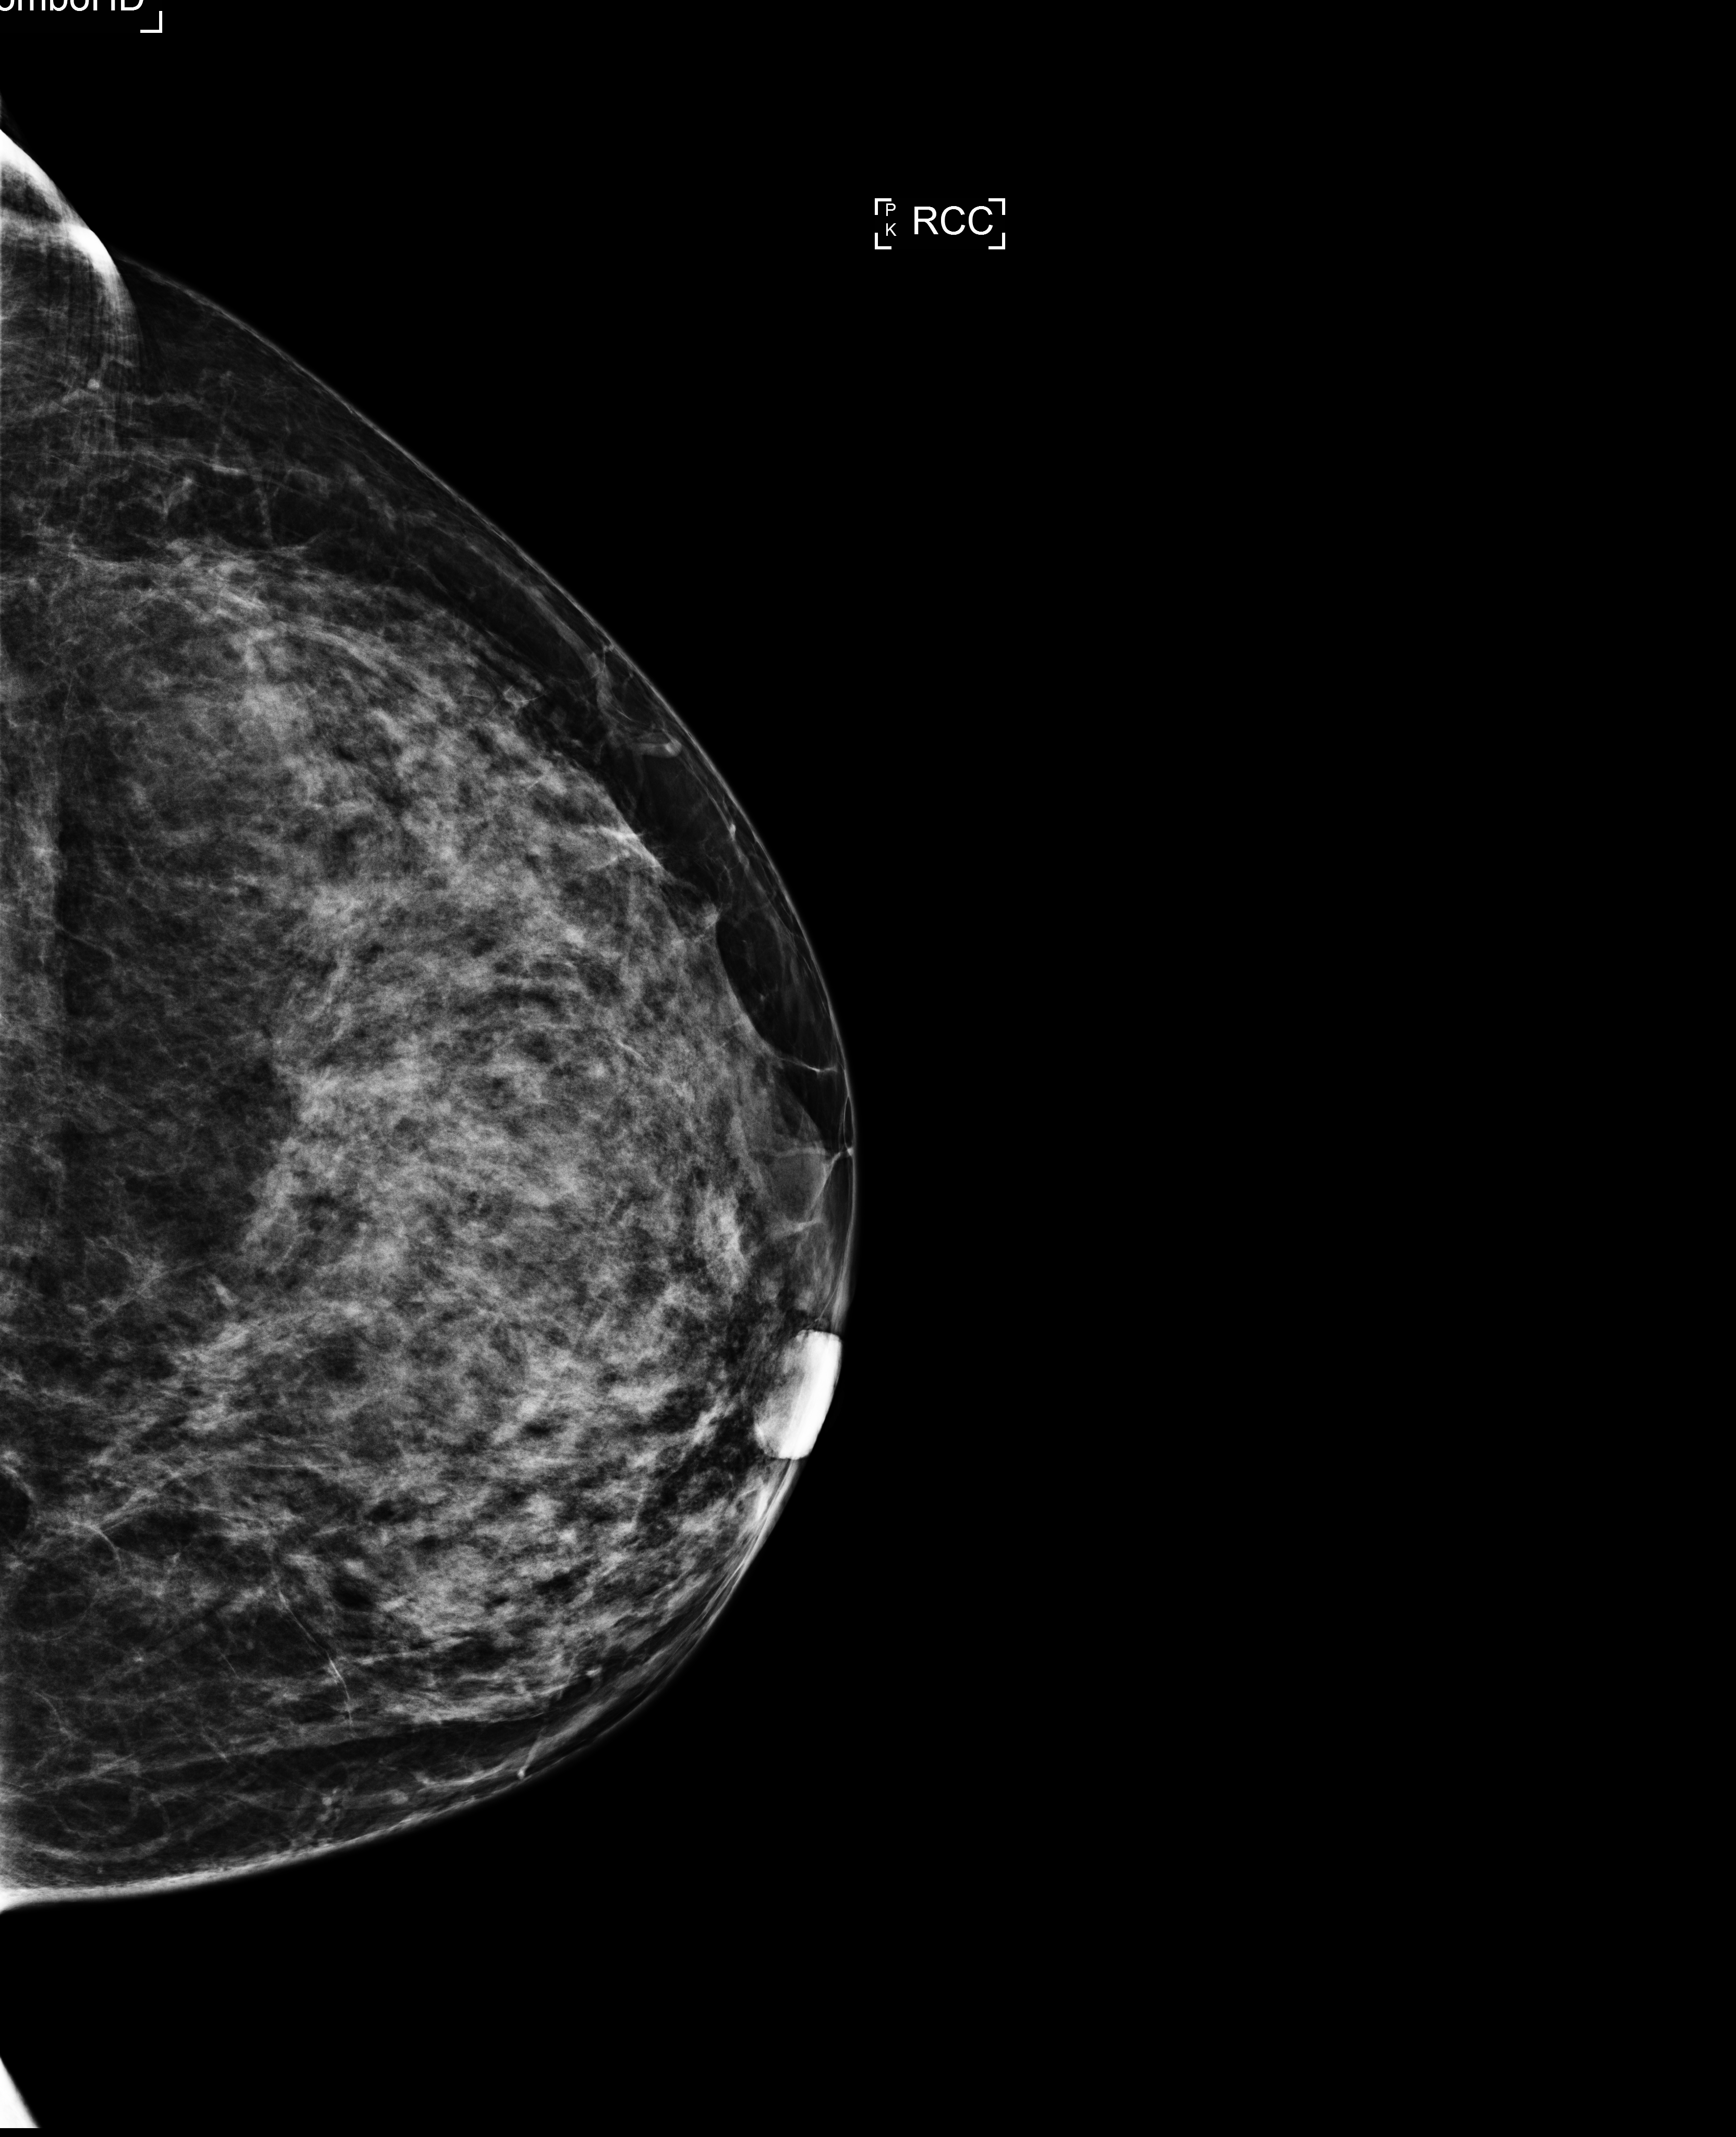
Annual screening mammography examination, compressed breast thickness 75 mm. Patient aged 43 years (female).
Image type: full-field digital mammogram. Breast: right. Projection: cranio-caudal projection.